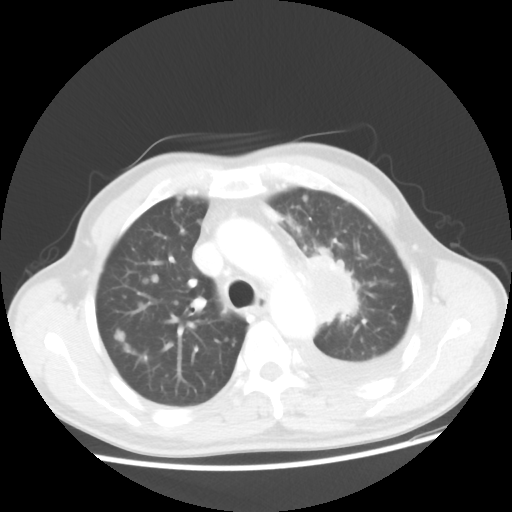
Chest CT, one axial slice. Position 34 of 48 along the scan axis. Lung window (W 1500 / L -600 HU). 5 mm slice thickness. 512 × 512 image matrix. Patient: male, 55 years. From the clinical record (not read from this slice): clinical TNM (as recorded): T2 N3 M1a.
Structures marked on this image (rectangle marked by the reading radiologist):
- lung tumour (recorded histology: squamous cell carcinoma): bounding box (x1, y1, x2, y2) in pixels: (304, 256, 359, 321)